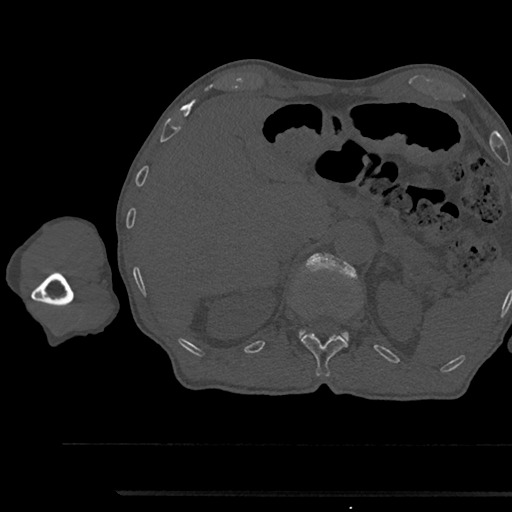
CT including the spine, one axial slice; position 687 of 797 along the scan axis; reconstruction kernel Br40s/3; bone window (W 1800 / L 400 HU); 512 × 512 image matrix. Male patient, age 79 years. From the clinical record (not read from this slice): primary cancer: prostate.
Outlined on this slice (semi-automatically segmented with operator editing):
- L1 vertebra: bounding box (x1, y1, x2, y2) in pixels: (298, 254, 358, 341)
- T12 vertebra: (301, 333, 348, 377)